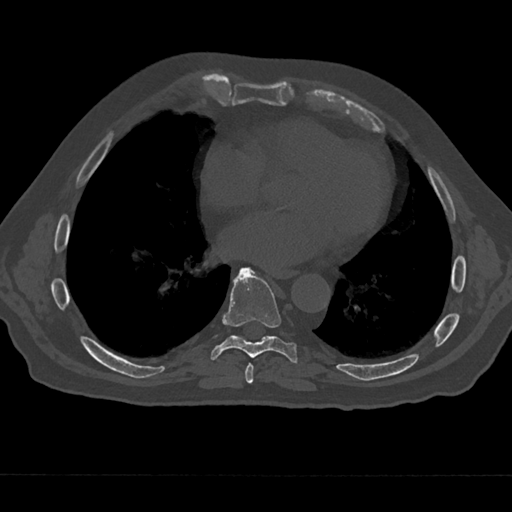
CT including the spine, one axial slice; position 315 of 797 along the scan axis; bone window (W 1800 / L 400 HU); 0.5 mm slice thickness; 512 × 512 image matrix, field of view 377 × 377 mm. Male patient, age 75 years. Case-level facts recorded for this patient, not image findings: primary cancer: renal; vertebrae with lytic lesions (as recorded): T4.
Structures marked on this image (semi-automatically segmented with operator editing):
- T7 vertebra: bounding box [x1, y1, x2, y2] px = [240, 362, 259, 384]
- T8 vertebra: [210, 268, 298, 364]